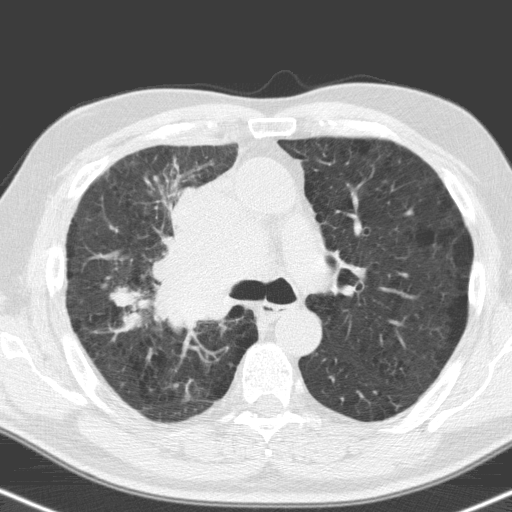
Low-dose screening chest CT, one axial slice. Slice 108 of 160 in the series (ordered by position). Lung window (W 1500 / L -600 HU). 3.2 mm slice thickness. 512 × 512 image matrix, field of view 324 × 324 mm.
Annotated regions visible in this slice (outlined manually by an expert reader):
- lesion 1 (tumor, hilum of right lung): bounding box (x1, y1, x2, y2) in pixels: (153, 185, 270, 323)
- lesion 2 (tumor, upper lobe of right lung): (113, 289, 134, 306)